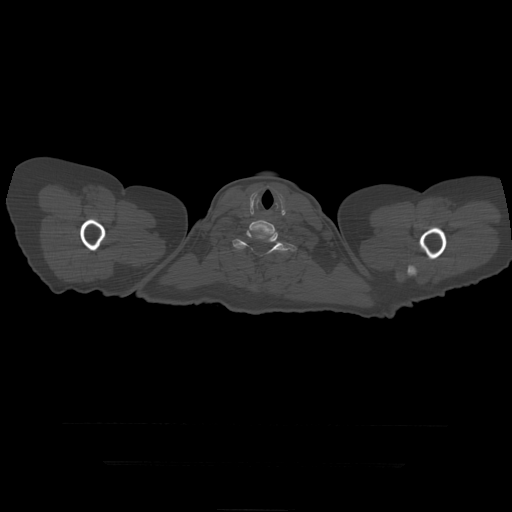
CT including the spine, one axial slice. Slice 393 of 399 in the series (ordered by position). Reconstruction kernel STANDARD. Bone window (W 1800 / L 400 HU). 1.25 mm slice thickness. 512 × 512 image matrix. Patient age 41 years. From the clinical record (not read from this slice): primary cancer: breast.
Outlined on this slice (semi-automatic segmentation, software-assisted and operator-edited):
- T1 vertebra: bounding box <233,230,297,256> (left, top, right, bottom; pixels)